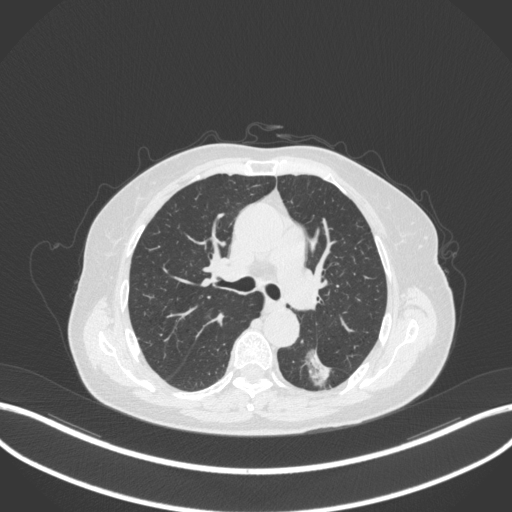
Chest CT, one axial slice. Slice 190 of 352 in the series (ordered by position). Reconstruction kernel B31f. 120 kVp. Lung window (W 1500 / L -600 HU). 1 mm slice thickness. 512 × 512 image matrix. Patient: female, 70 years. From the clinical record (not read from this slice): clinical TNM (as recorded): T1c N0 M0.
Structures marked on this image (rectangle marked by the reading radiologist):
- lung tumour (recorded histology: adenocarcinoma): bounding box <303,346,333,393> (left, top, right, bottom; pixels)